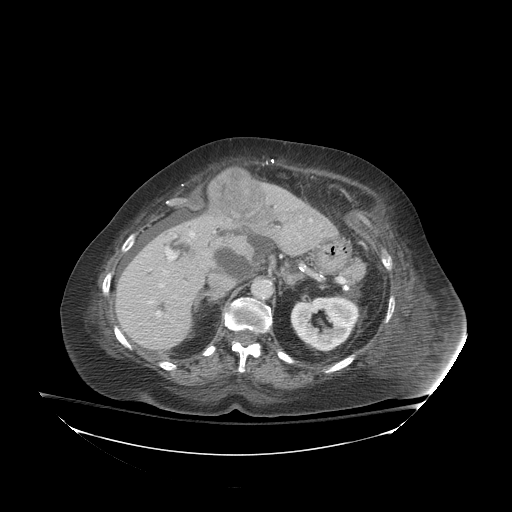
Contrast-enhanced abdominal CT (liver protocol), one axial slice; position 52 of 81 along the scan axis; 140 kVp; soft-tissue window (W 400 / L 40 HU); 512 × 512 image matrix, field of view 500 × 500 mm. Case-level facts recorded for this patient, not image findings: diagnosis: hepatocellular carcinoma (patient treated with transarterial chemoembolisation; whether this scan precedes or follows treatment is not stated here); TNM stage (as recorded): Stage-I; Child-Pugh class: B.
Outlined on this slice (semi-automatically segmented with operator editing):
- liver parenchyma outside the tumour (the mass and vessels are separate outlines, so this box may not span the whole liver): bounding box (x1, y1, x2, y2) in pixels: (116, 182, 334, 350)
- mass: (208, 166, 267, 225)
- liver vessels: (148, 219, 312, 316)